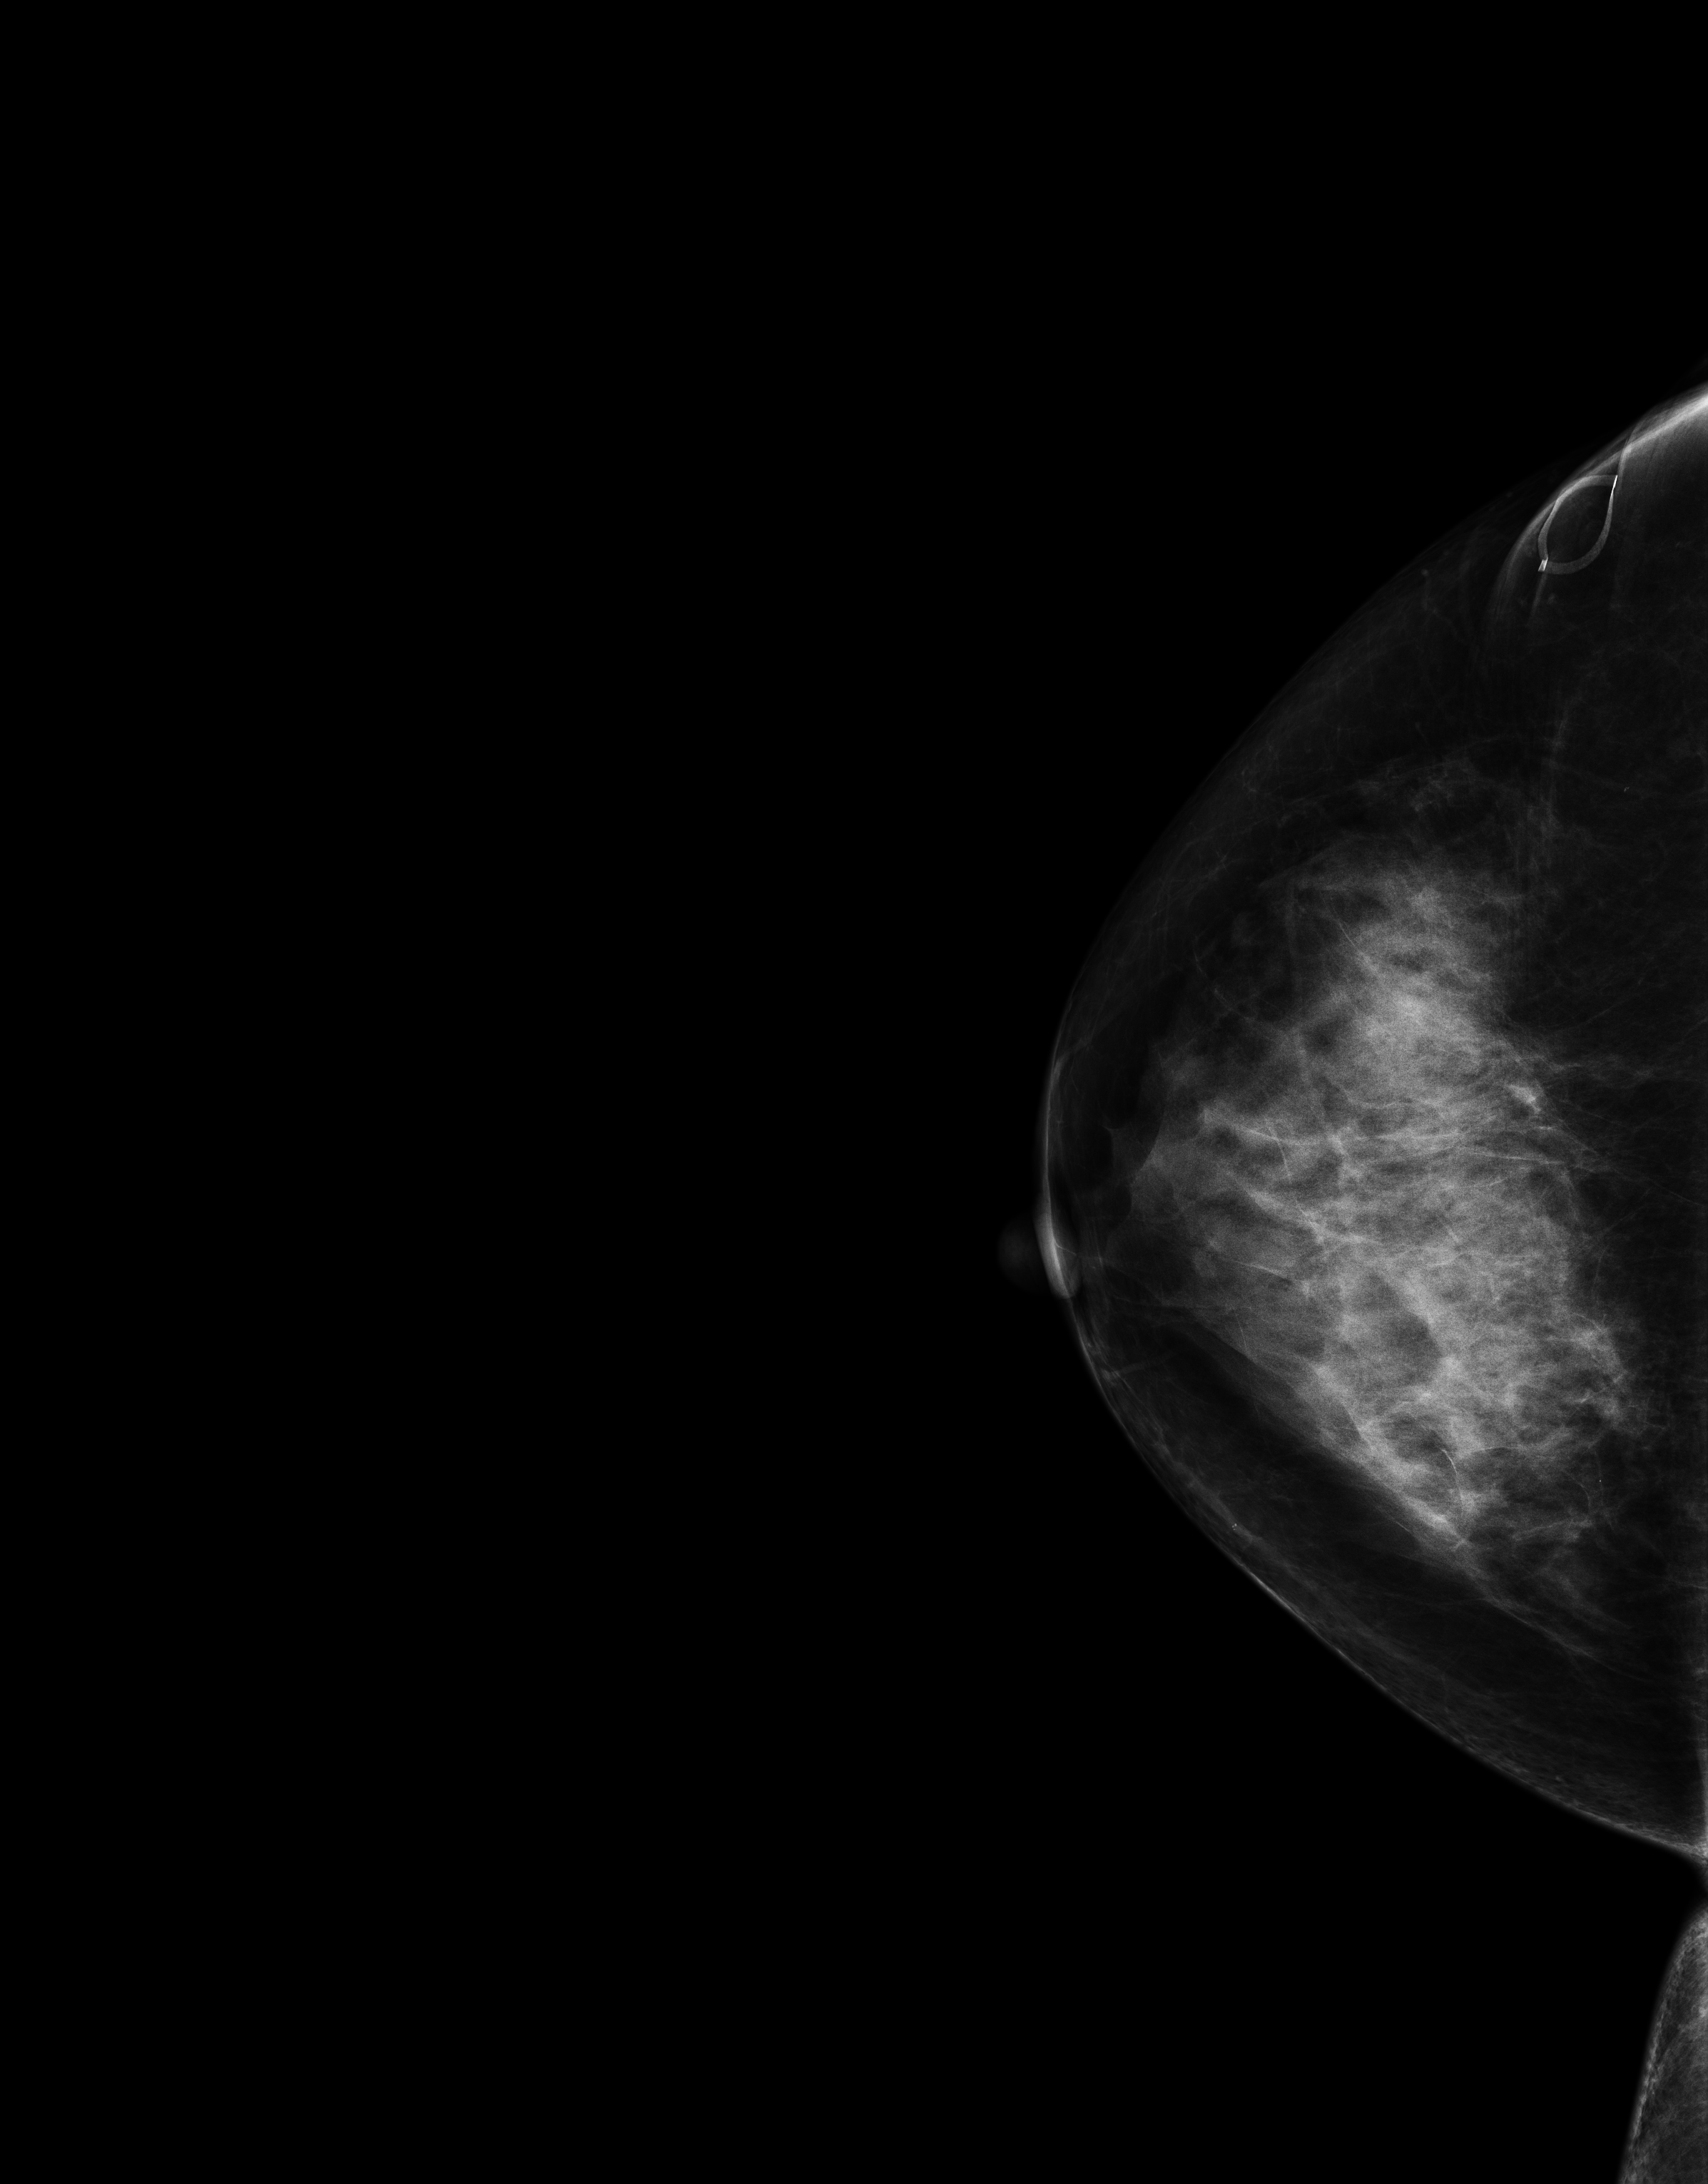
Full-field digital mammogram (FFDM); right breast; CC view; annual screening mammography examination; system: Senographe Essential ADS_56.21.3. Patient aged 67 years (female).
- breast density at the screening exam (both breasts): heterogeneously dense (BI-RADS density category c)
- final BI-RADS category for the screening round (tomosynthesis exam, both breasts): category 1
- recall: no recall after this screen